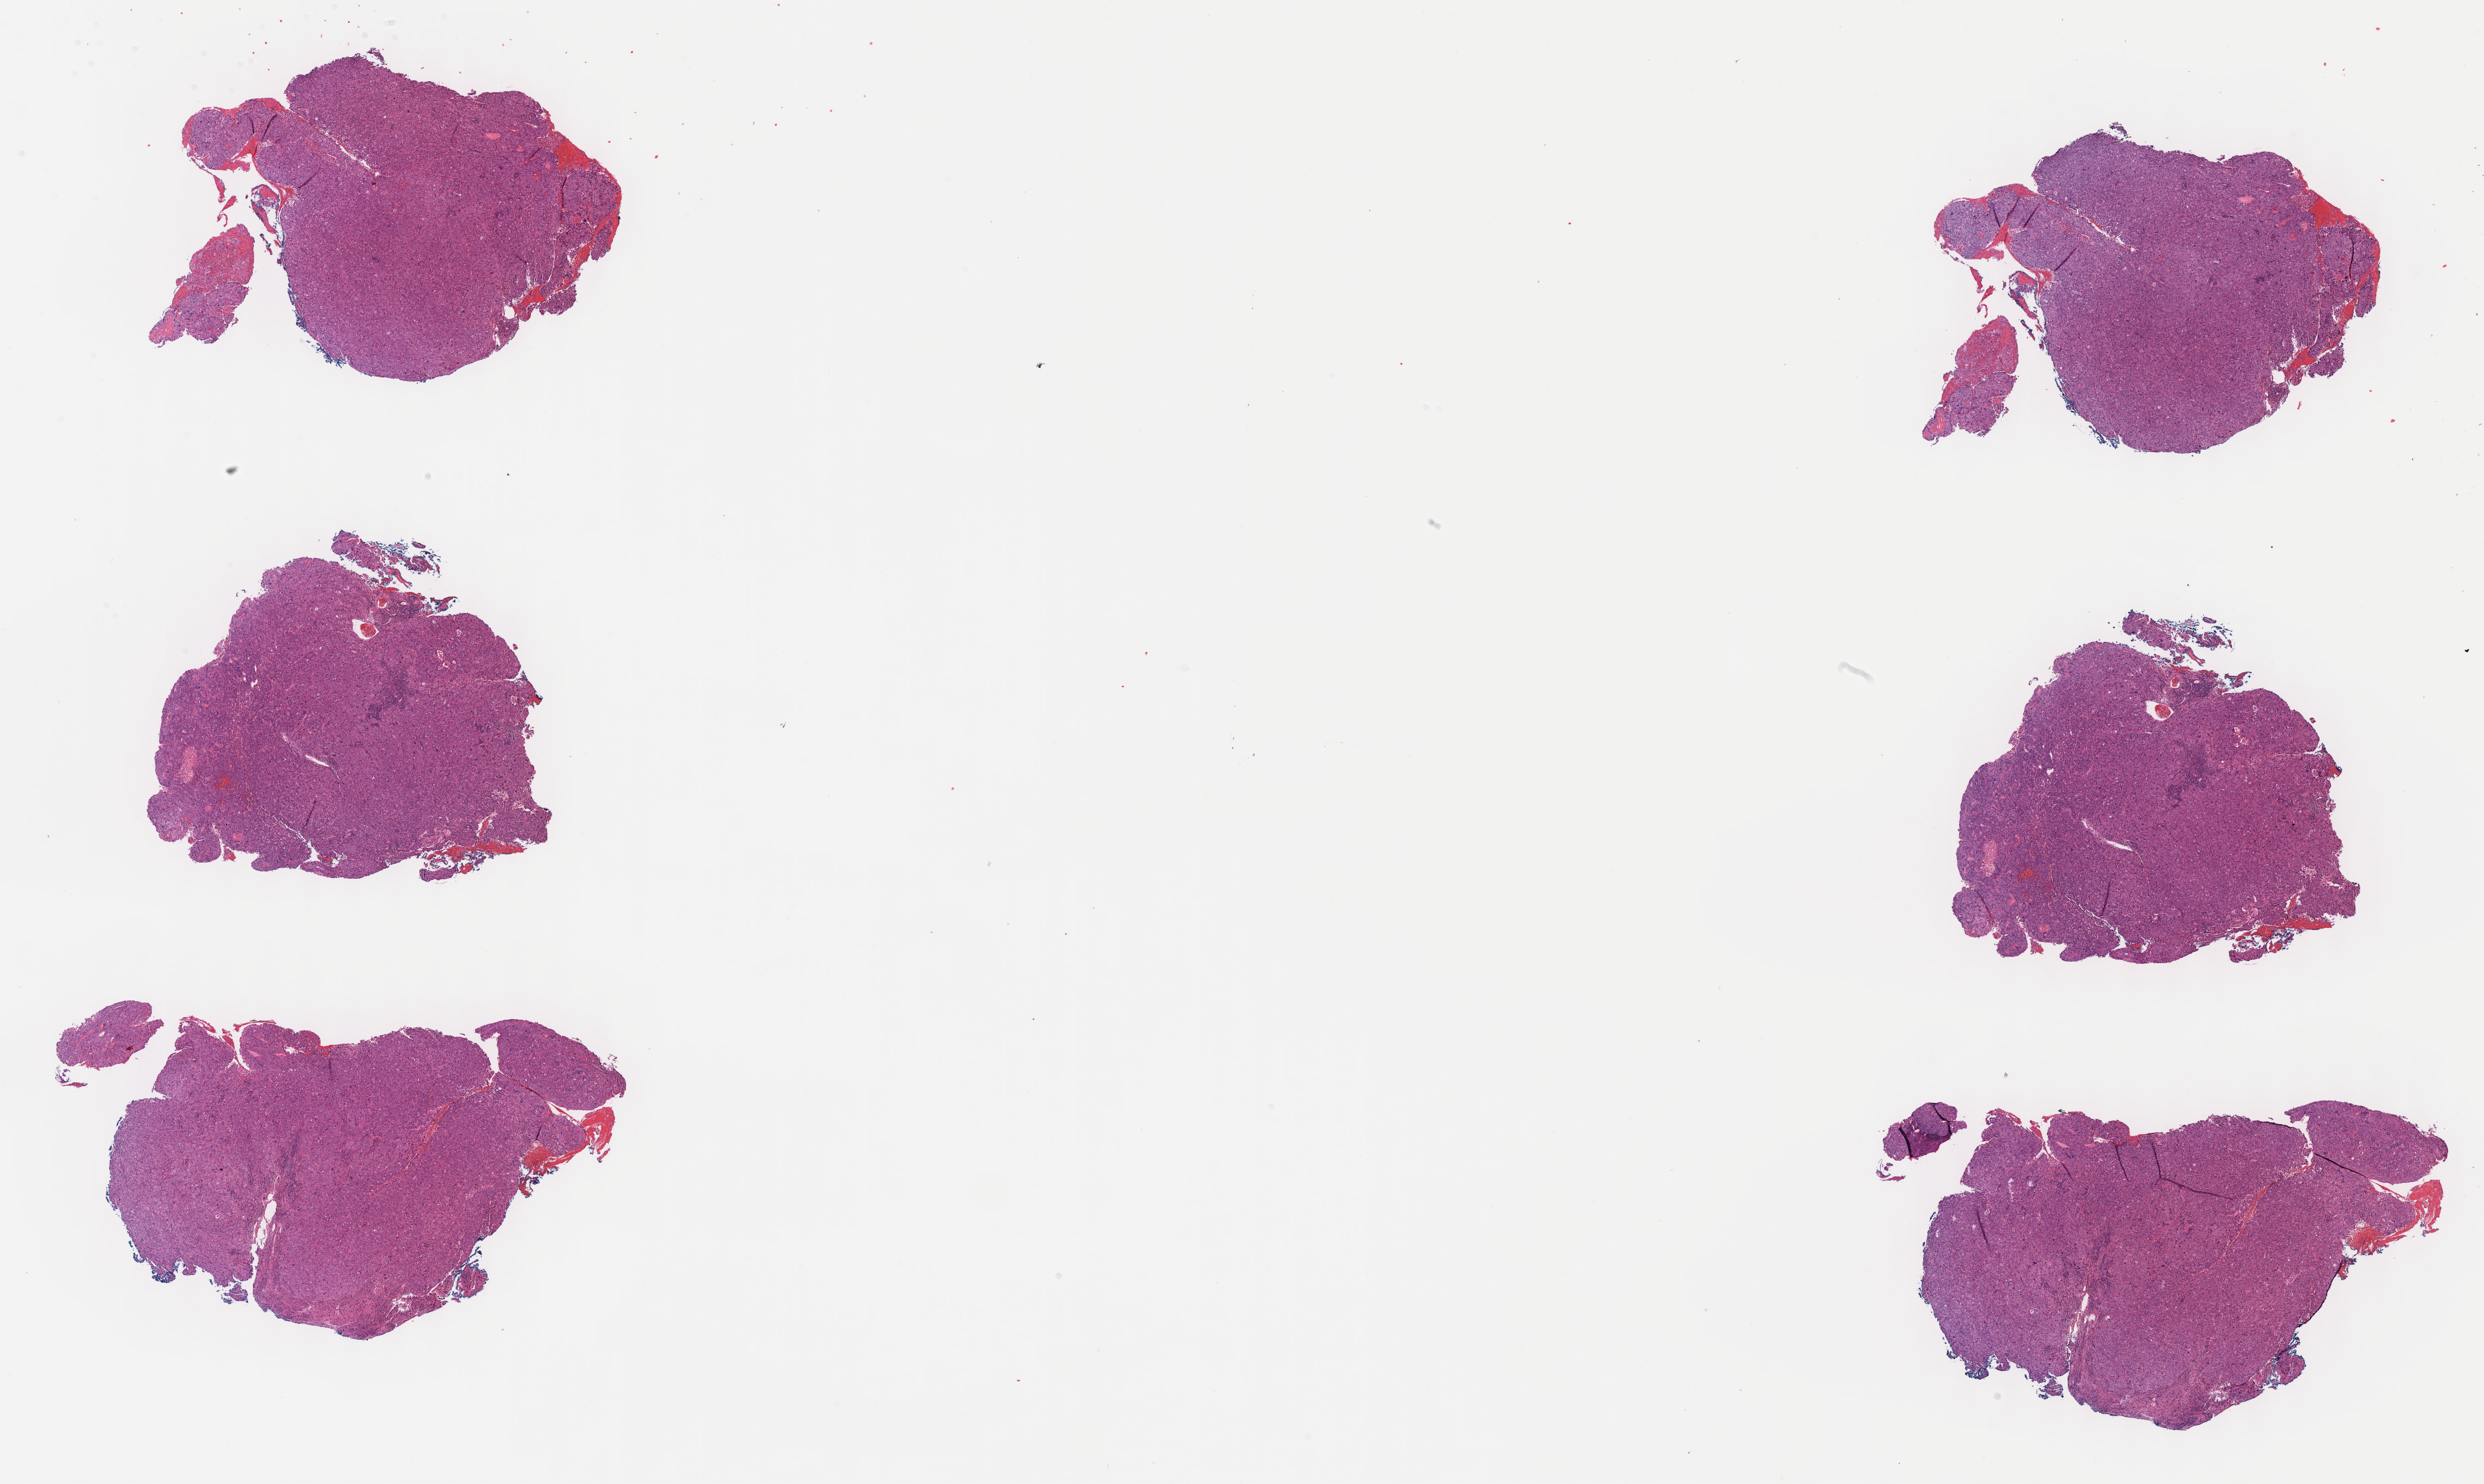
Whole-slide histology image, H&E — low-resolution overview of the scanned area, about 30.2 x 18.0 mm (from a 40x scan); formalin-fixed paraffin-embedded (FFPE) diagnostic section; primary tumour sample from the cervix. Patient: female, age at initial diagnosis 28 years. Histologic grade: G3 (poorly differentiated).
FIGO stage: IIA. Pathologic diagnosis: Squamous cell carcinoma, NOS (cervix uteri).